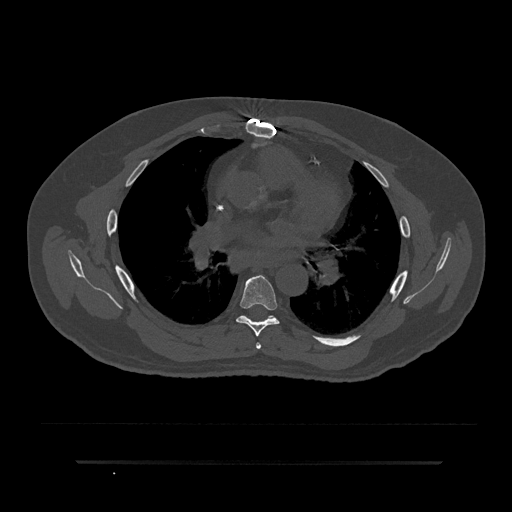
CT including the spine, one axial slice; position 522 of 797 along the scan axis; bone window (W 1800 / L 400 HU); 0.5 mm slice thickness; 512 × 512 image matrix. Patient: male, 59 years. Case-level facts recorded for this patient, not image findings: primary cancer: bile ducts; vertebrae with lytic lesions (as recorded): T10.
Annotated regions visible in this slice (semi-automatic segmentation, software-assisted and operator-edited):
- T5 vertebra: bounding box (x1, y1, x2, y2) in pixels: (256, 343, 261, 349)
- T6 vertebra: (236, 275, 280, 337)